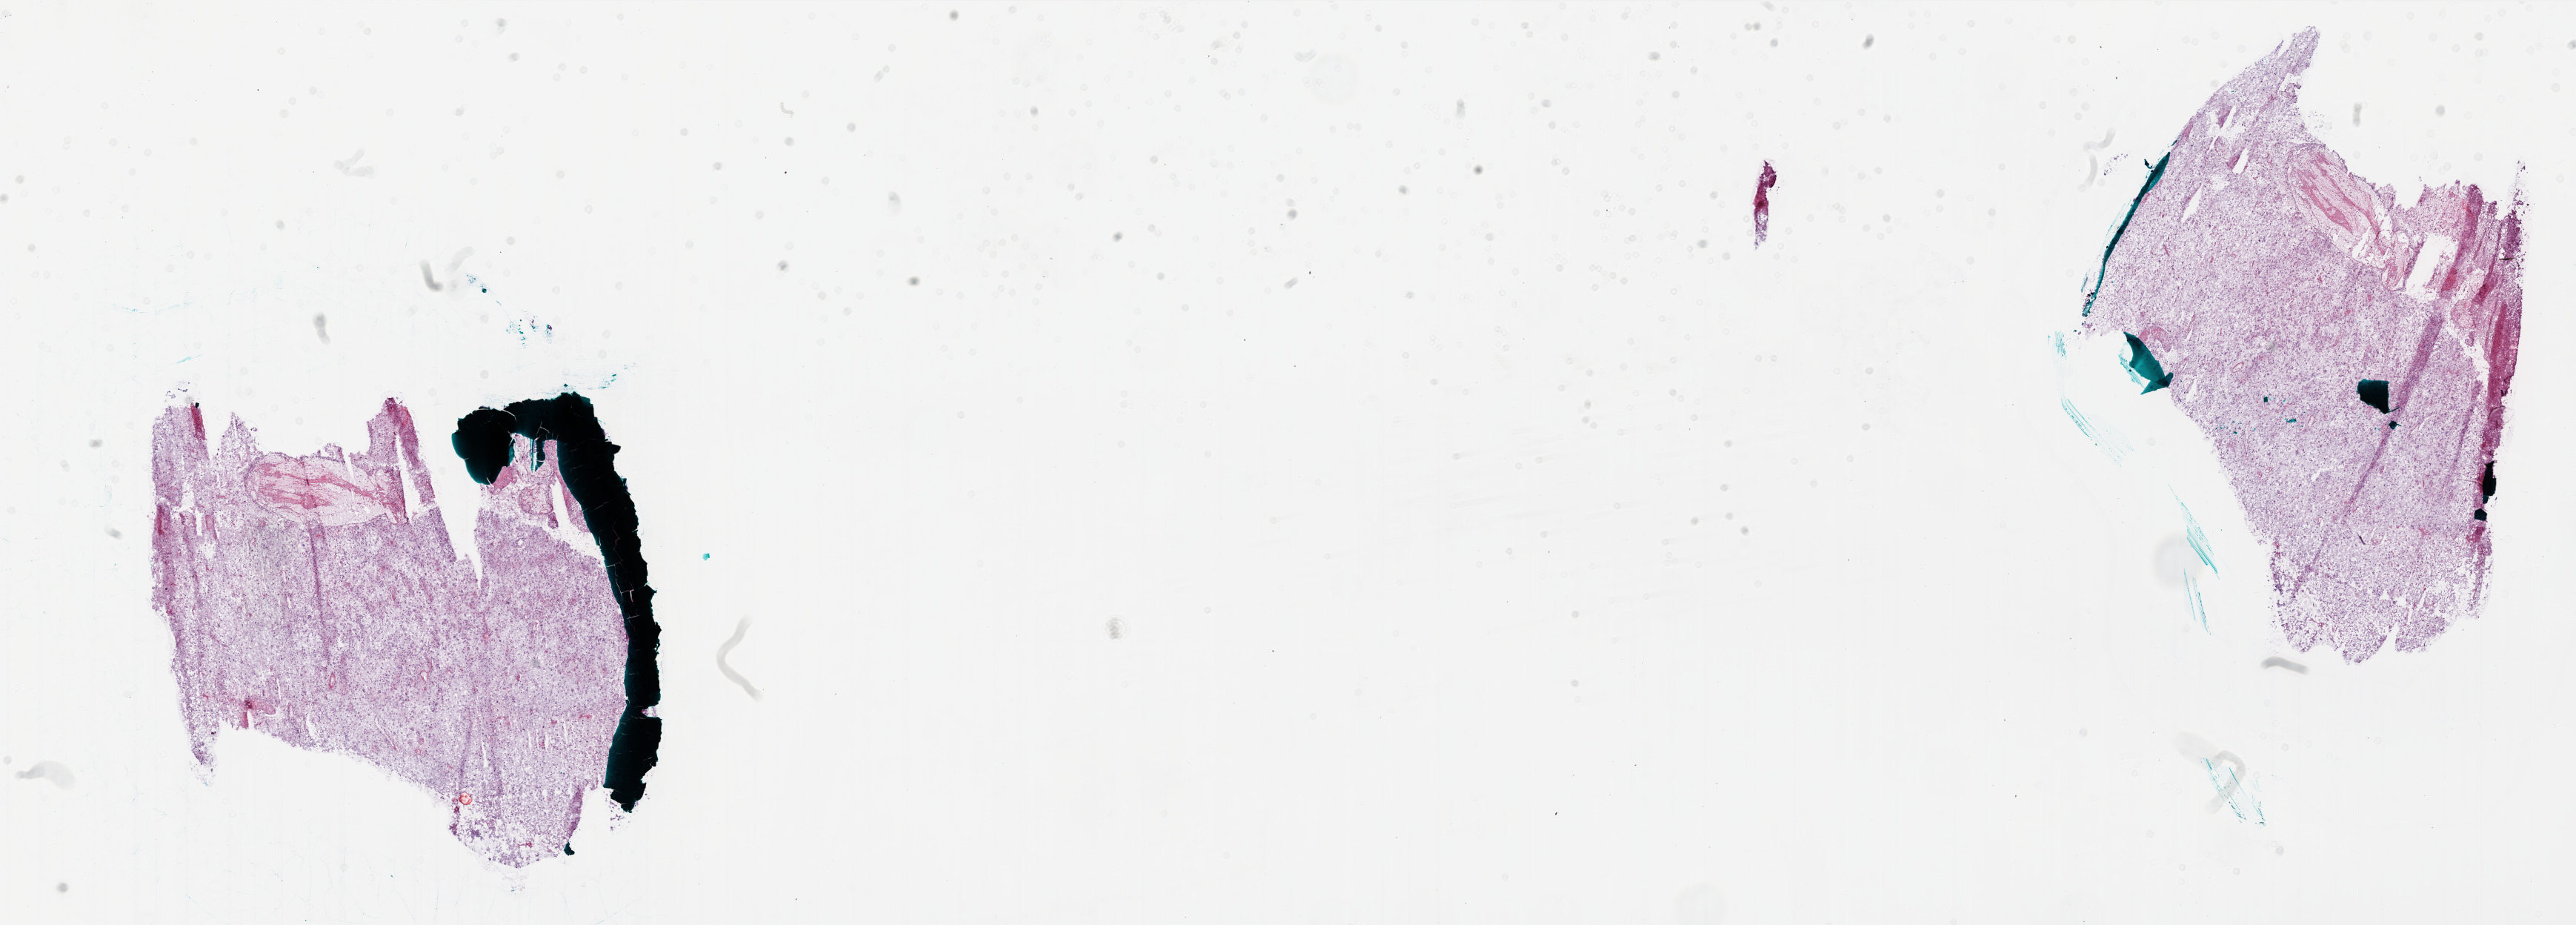
Whole-slide histology image, H&E-stained — whole scanned area (about 28.0 x 10.0 mm) shown as a low-resolution overview; frozen section; brain, primary tumour sample. Patient: female, age at initial diagnosis 65 years.
Pathologic diagnosis: Glioblastoma.